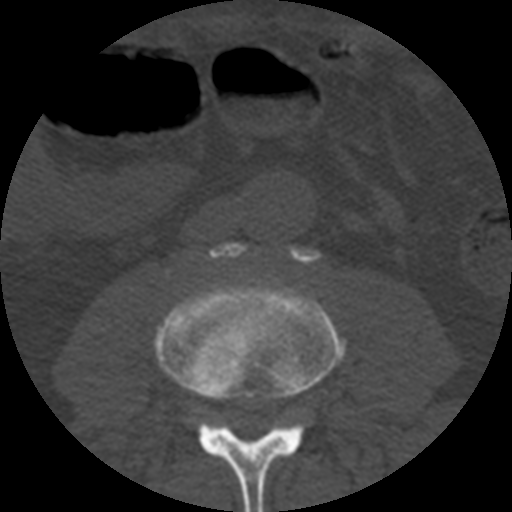
CT including the spine, one axial slice. Position 113 of 508 along the scan axis. Reconstruction kernel STANDARD. 120 kVp. Bone window (W 1800 / L 400 HU). 1.25 mm slice thickness. 512 × 512 image matrix, field of view 160 × 160 mm. Patient age 57 years. From the clinical record (not read from this slice): primary cancer: prostate.
Structures marked on this image (semi-automatic segmentation, software-assisted and operator-edited):
- L3 vertebra: bounding box [x1, y1, x2, y2] px = [154, 281, 345, 512]
- L4 vertebra: [211, 242, 320, 264]